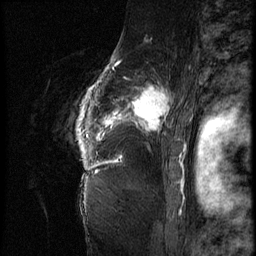
Breast MRI (dynamic contrast-enhanced), one sagittal slice; position 53 of 62 along the scan axis; 3 images stored at this slice position (order not interpretable as contrast timing); 1.5 T; TE 4.2 ms, TR 9 ms; 256 × 256 image matrix, field of view 180 × 180 mm. Female patient, age 56 years. Case-level facts recorded for this patient, not image findings: setting: breast cancer imaged before/during neoadjuvant chemotherapy; receptor status: HER2-positive.
Outlined on this slice (semi-automatic segmentation, software-assisted and operator-edited):
- analysis volume of interest (the breast-tissue region the enhancement analysis was run in; not a lesion): bounding box [x1, y1, x2, y2] px = [84, 75, 181, 153]
- tumour enhancement mask (voxels above the 140 % enhancement threshold inside the analysis volume of interest): [84, 85, 172, 140]